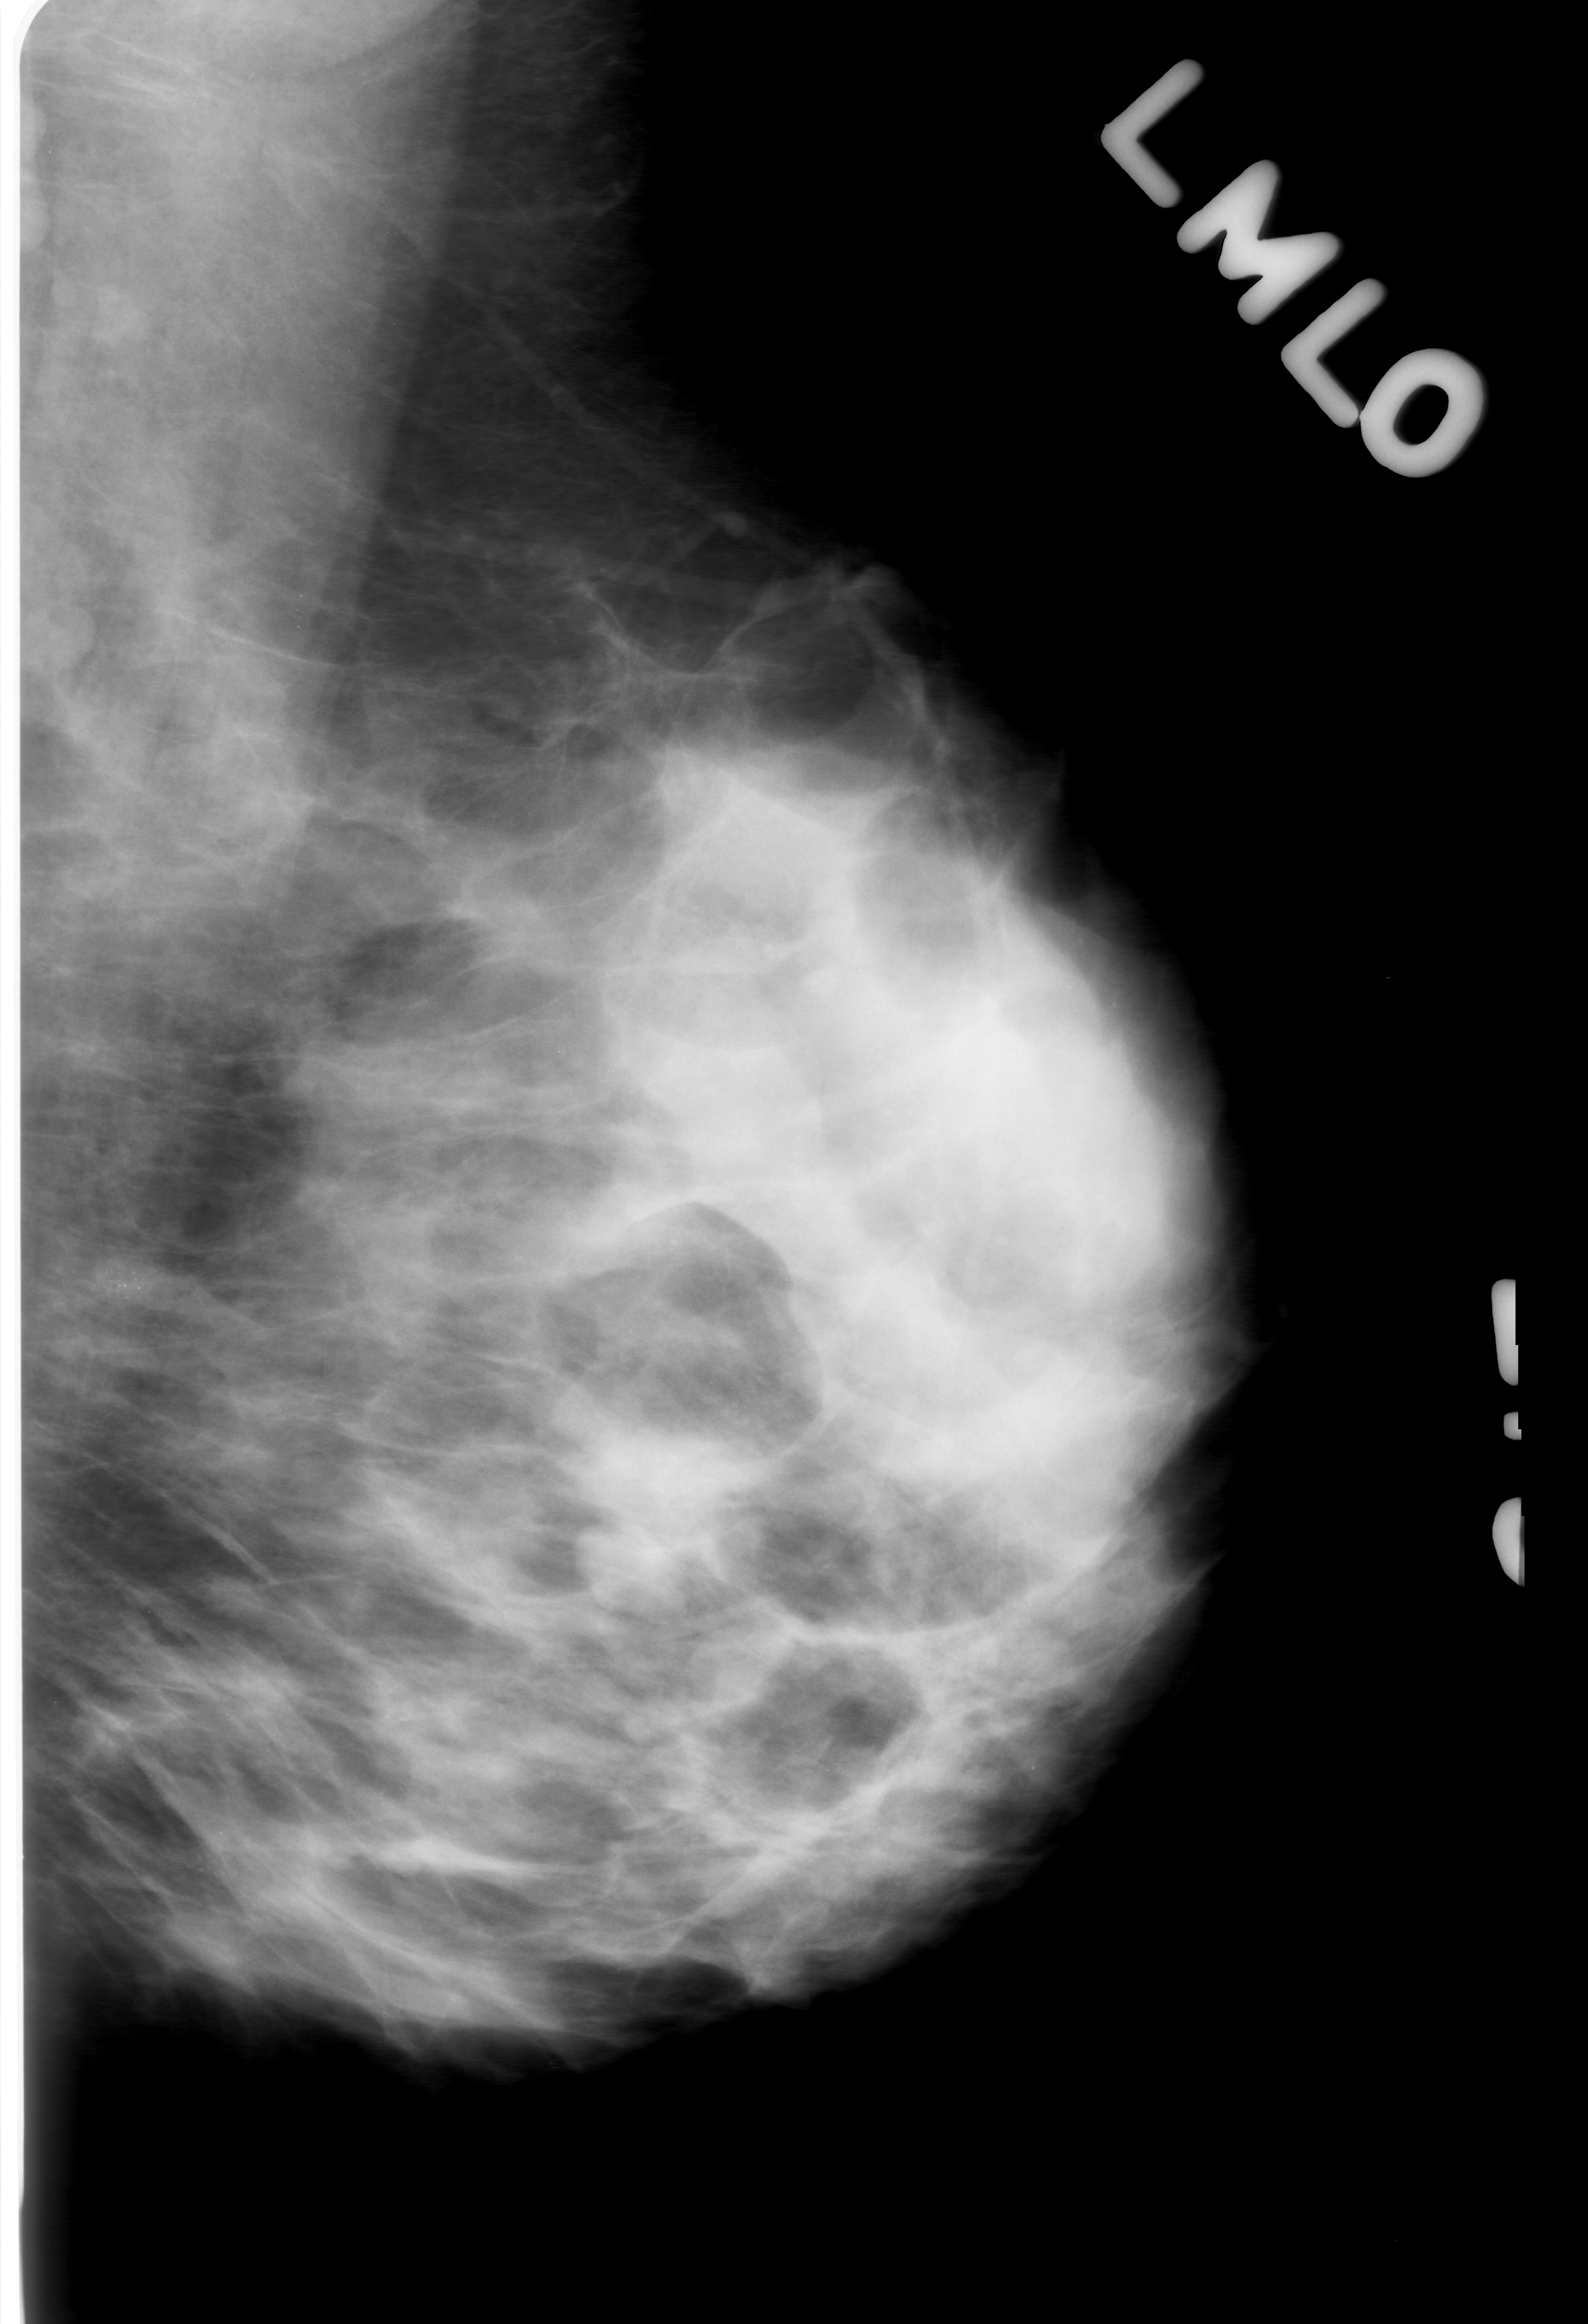
Digitized screen-film mammogram; left breast; mediolateral oblique (MLO) view; BI-RADS breast density category 3 (scale 1–4).
Radiologist-marked abnormalities on this image: calcifications, morphology round and regular / pleomorphic, distribution clustered; BI-RADS assessment category 0; subtlety rating 3 on a 1 (subtle) to 5 (obvious) scale; pathology (as recorded): benign.